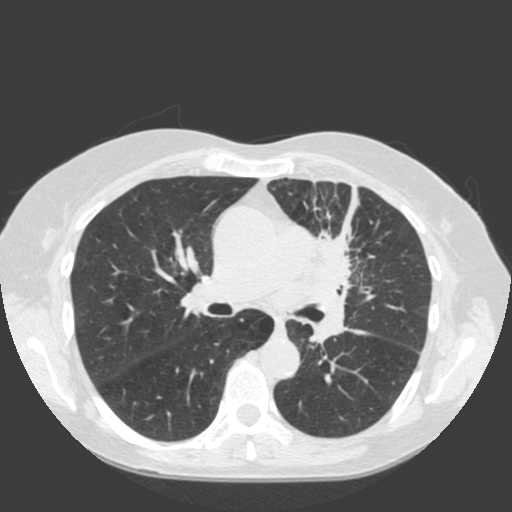
Chest CT (low-dose screening protocol), one axial image; first (baseline) screen; lung window (W 1500 / L -600 HU); standard (soft-tissue) reconstruction kernel (C); slice 72 of 184 in the series. Female participant, aged 66 years at enrolment.
Lesion marked by an expert reader, bounding box [x1, y1, x2, y2] px = [277, 204, 402, 317]. The exam's reader record, not a measurement of the box and not confirmed to be the same lesion: non-calcified nodule or mass ≥4 mm, left upper lobe, 61 × 45 mm, spiculated (stellate) margins, soft tissue attenuation. Participant outcome: lung cancer diagnosed 19 days after this screen — squamous cell carcinoma, keratinizing, NOS, left upper lobe, left hilum, mediastinum, left main stem bronchus, other location, poorly differentiated (G3), stage IIIB (AJCC 6th edition), 60 mm at pathology.